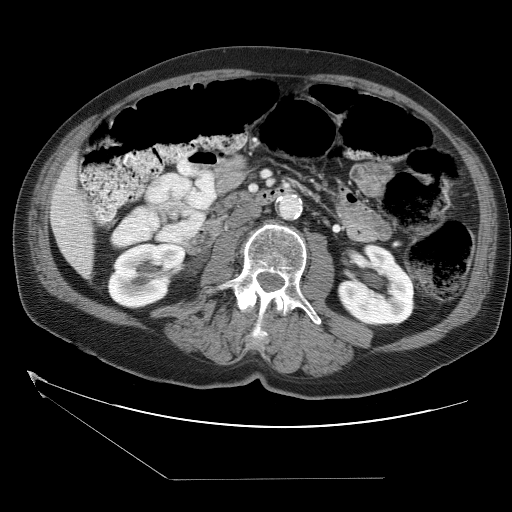
Contrast-enhanced abdominal CT (liver protocol), one axial slice; slice 5 of 38 in the series (ordered by position); 120 kVp; soft-tissue window (W 400 / L 40 HU); 5 mm slice thickness; 512 × 512 image matrix, field of view 400 × 400 mm. Case-level facts recorded for this patient, not image findings: diagnosis: hepatocellular carcinoma (patient treated with transarterial chemoembolisation; whether this scan precedes or follows treatment is not stated here); TNM stage (as recorded): Stage-II; Child-Pugh class: A; tumour differentiation: moderately differentiated; tumour nodularity: multinodular.
Outlined on this slice (semi-automatically segmented with operator editing):
- liver parenchyma outside the tumour (the mass and vessels are separate outlines, so this box may not span the whole liver): bounding box (x1, y1, x2, y2) in pixels: (50, 156, 94, 277)
- liver vessels: (60, 220, 65, 224)